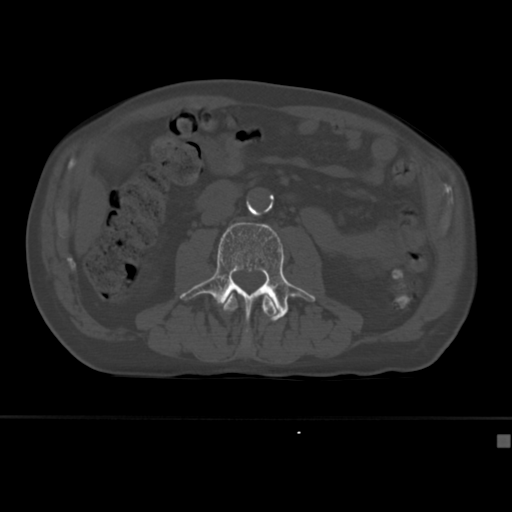
CT including the spine, one axial slice; position 132 of 430 along the scan axis; reconstruction kernel Br40s; bone window (W 1800 / L 400 HU); 1.5 mm slice thickness; 512 × 512 image matrix. Male patient, age 64 years. Case-level facts recorded for this patient, not image findings: primary cancer: uterus; vertebrae with lytic lesions (as recorded): T1, T4, T5, T7, L5.
Outlined on this slice (semi-automatically segmented with operator editing):
- L2 vertebra: bounding box (x1, y1, x2, y2) in pixels: (223, 292, 279, 349)
- L3 vertebra: (179, 222, 316, 335)